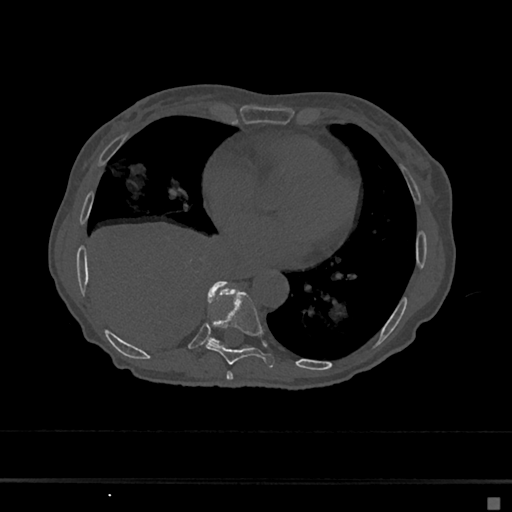
CT including the spine, one axial slice. Slice 312 of 797 in the series (ordered by position). 120 kVp. Bone window (W 1800 / L 400 HU). 0.5 mm slice thickness. 512 × 512 image matrix, field of view 360 × 360 mm. Female patient, age 68 years. Case-level facts recorded for this patient, not image findings: primary cancer: renal.
Annotated regions visible in this slice (semi-automatically segmented with operator editing):
- T7 vertebra: bounding box (x1, y1, x2, y2) in pixels: (226, 371, 233, 380)
- T8 vertebra: (206, 290, 275, 368)
- T9 vertebra: (208, 281, 226, 345)